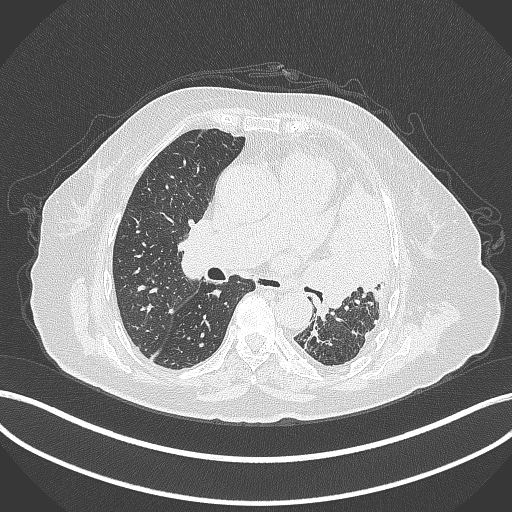
Chest CT, one axial slice. Position 206 of 399 along the scan axis. Lung window (W 1500 / L -600 HU). 1 mm slice thickness. 512 × 512 image matrix, field of view 400 × 400 mm. Female patient, age 75 years. From the clinical record (not read from this slice): clinical TNM (as recorded): T3 N3 M1.
Outlined on this slice (bounding box drawn by a radiologist):
- lung tumour (recorded histology: adenocarcinoma): bounding box <298,178,401,314> (left, top, right, bottom; pixels)